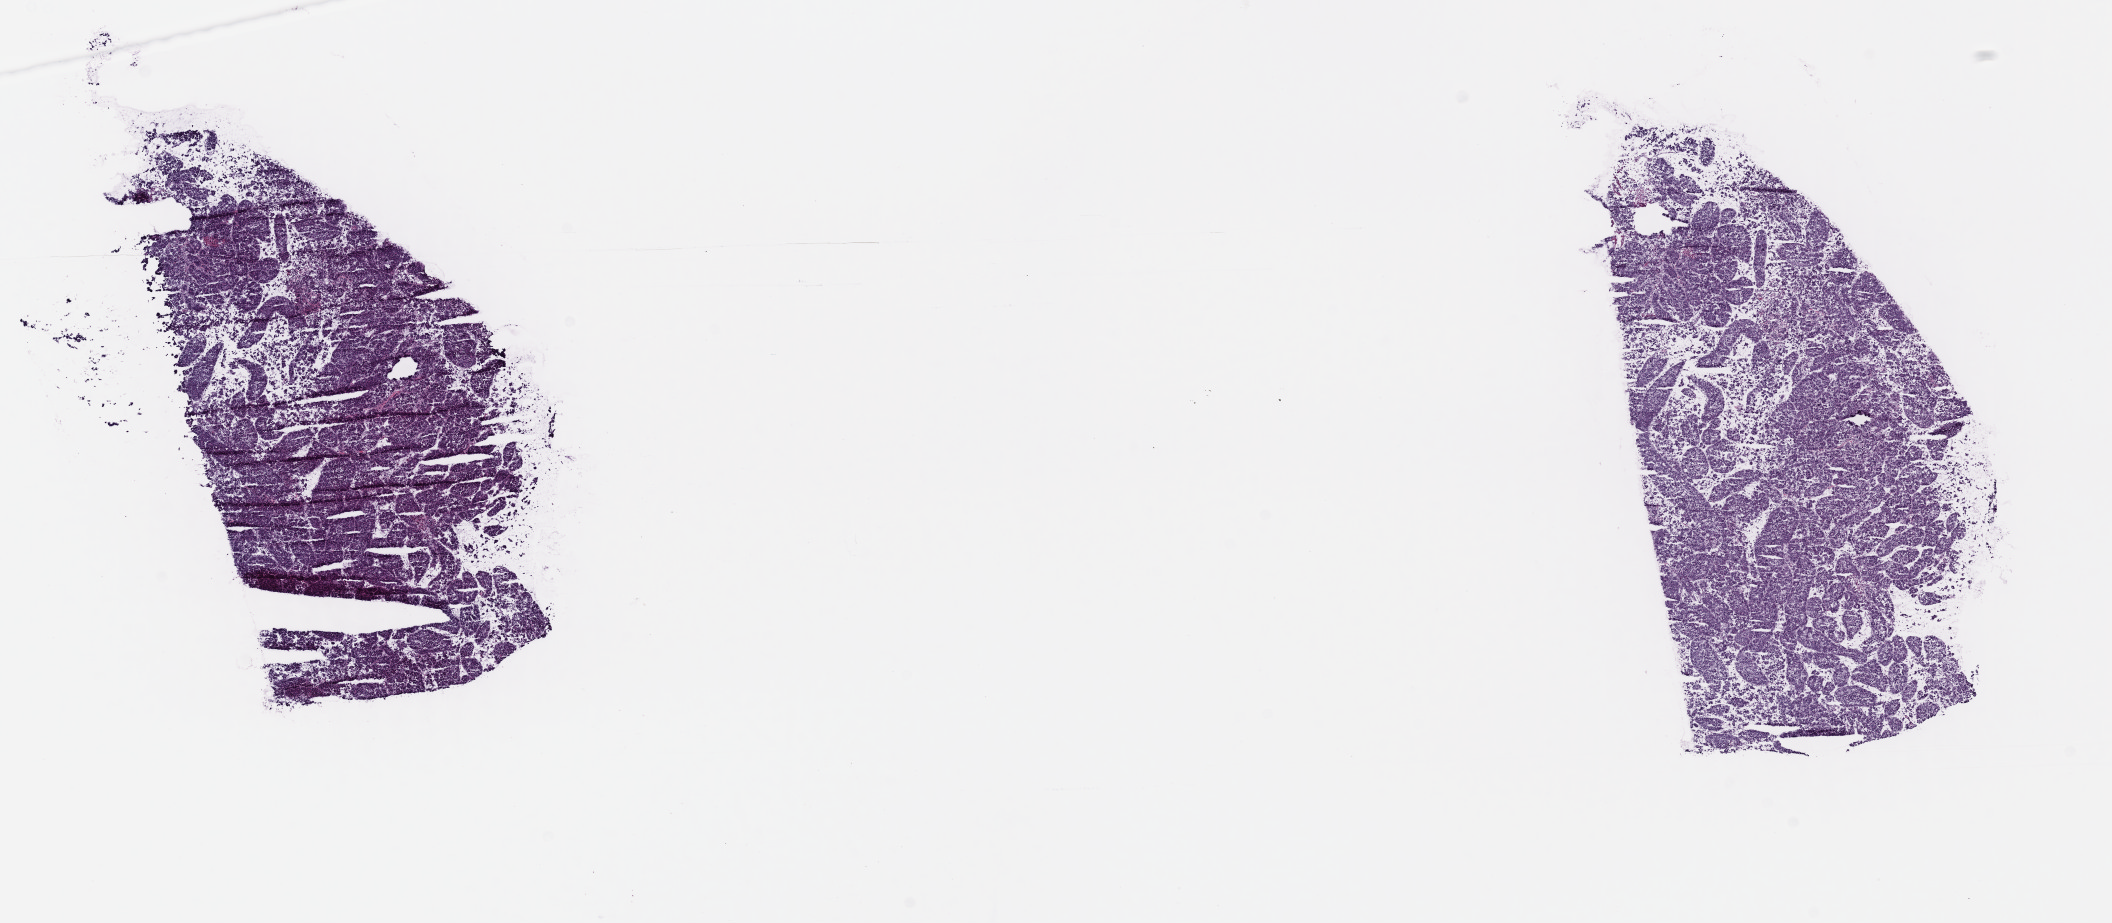
H&E-stained whole-slide image, a low-resolution overview of the entire scanned area, about 16.7 x 7.3 mm, frozen section, sample: primary tumour, liver. Female patient; age at initial diagnosis 62 years. Histologic grade: G2 (moderately differentiated). Slide review estimates, as recorded: tumour cells 94%, tumour nuclei 95%, normal cells 0%, stromal cells 4%, necrosis 2%. Inflammatory infiltration, as recorded: lymphocyte infiltration 1%, monocyte infiltration 1%, neutrophil infiltration 0%.
Diagnosis: Hepatocellular carcinoma, NOS. TNM: T3 NX M0. AJCC pathologic stage: IIIA (6th edition).